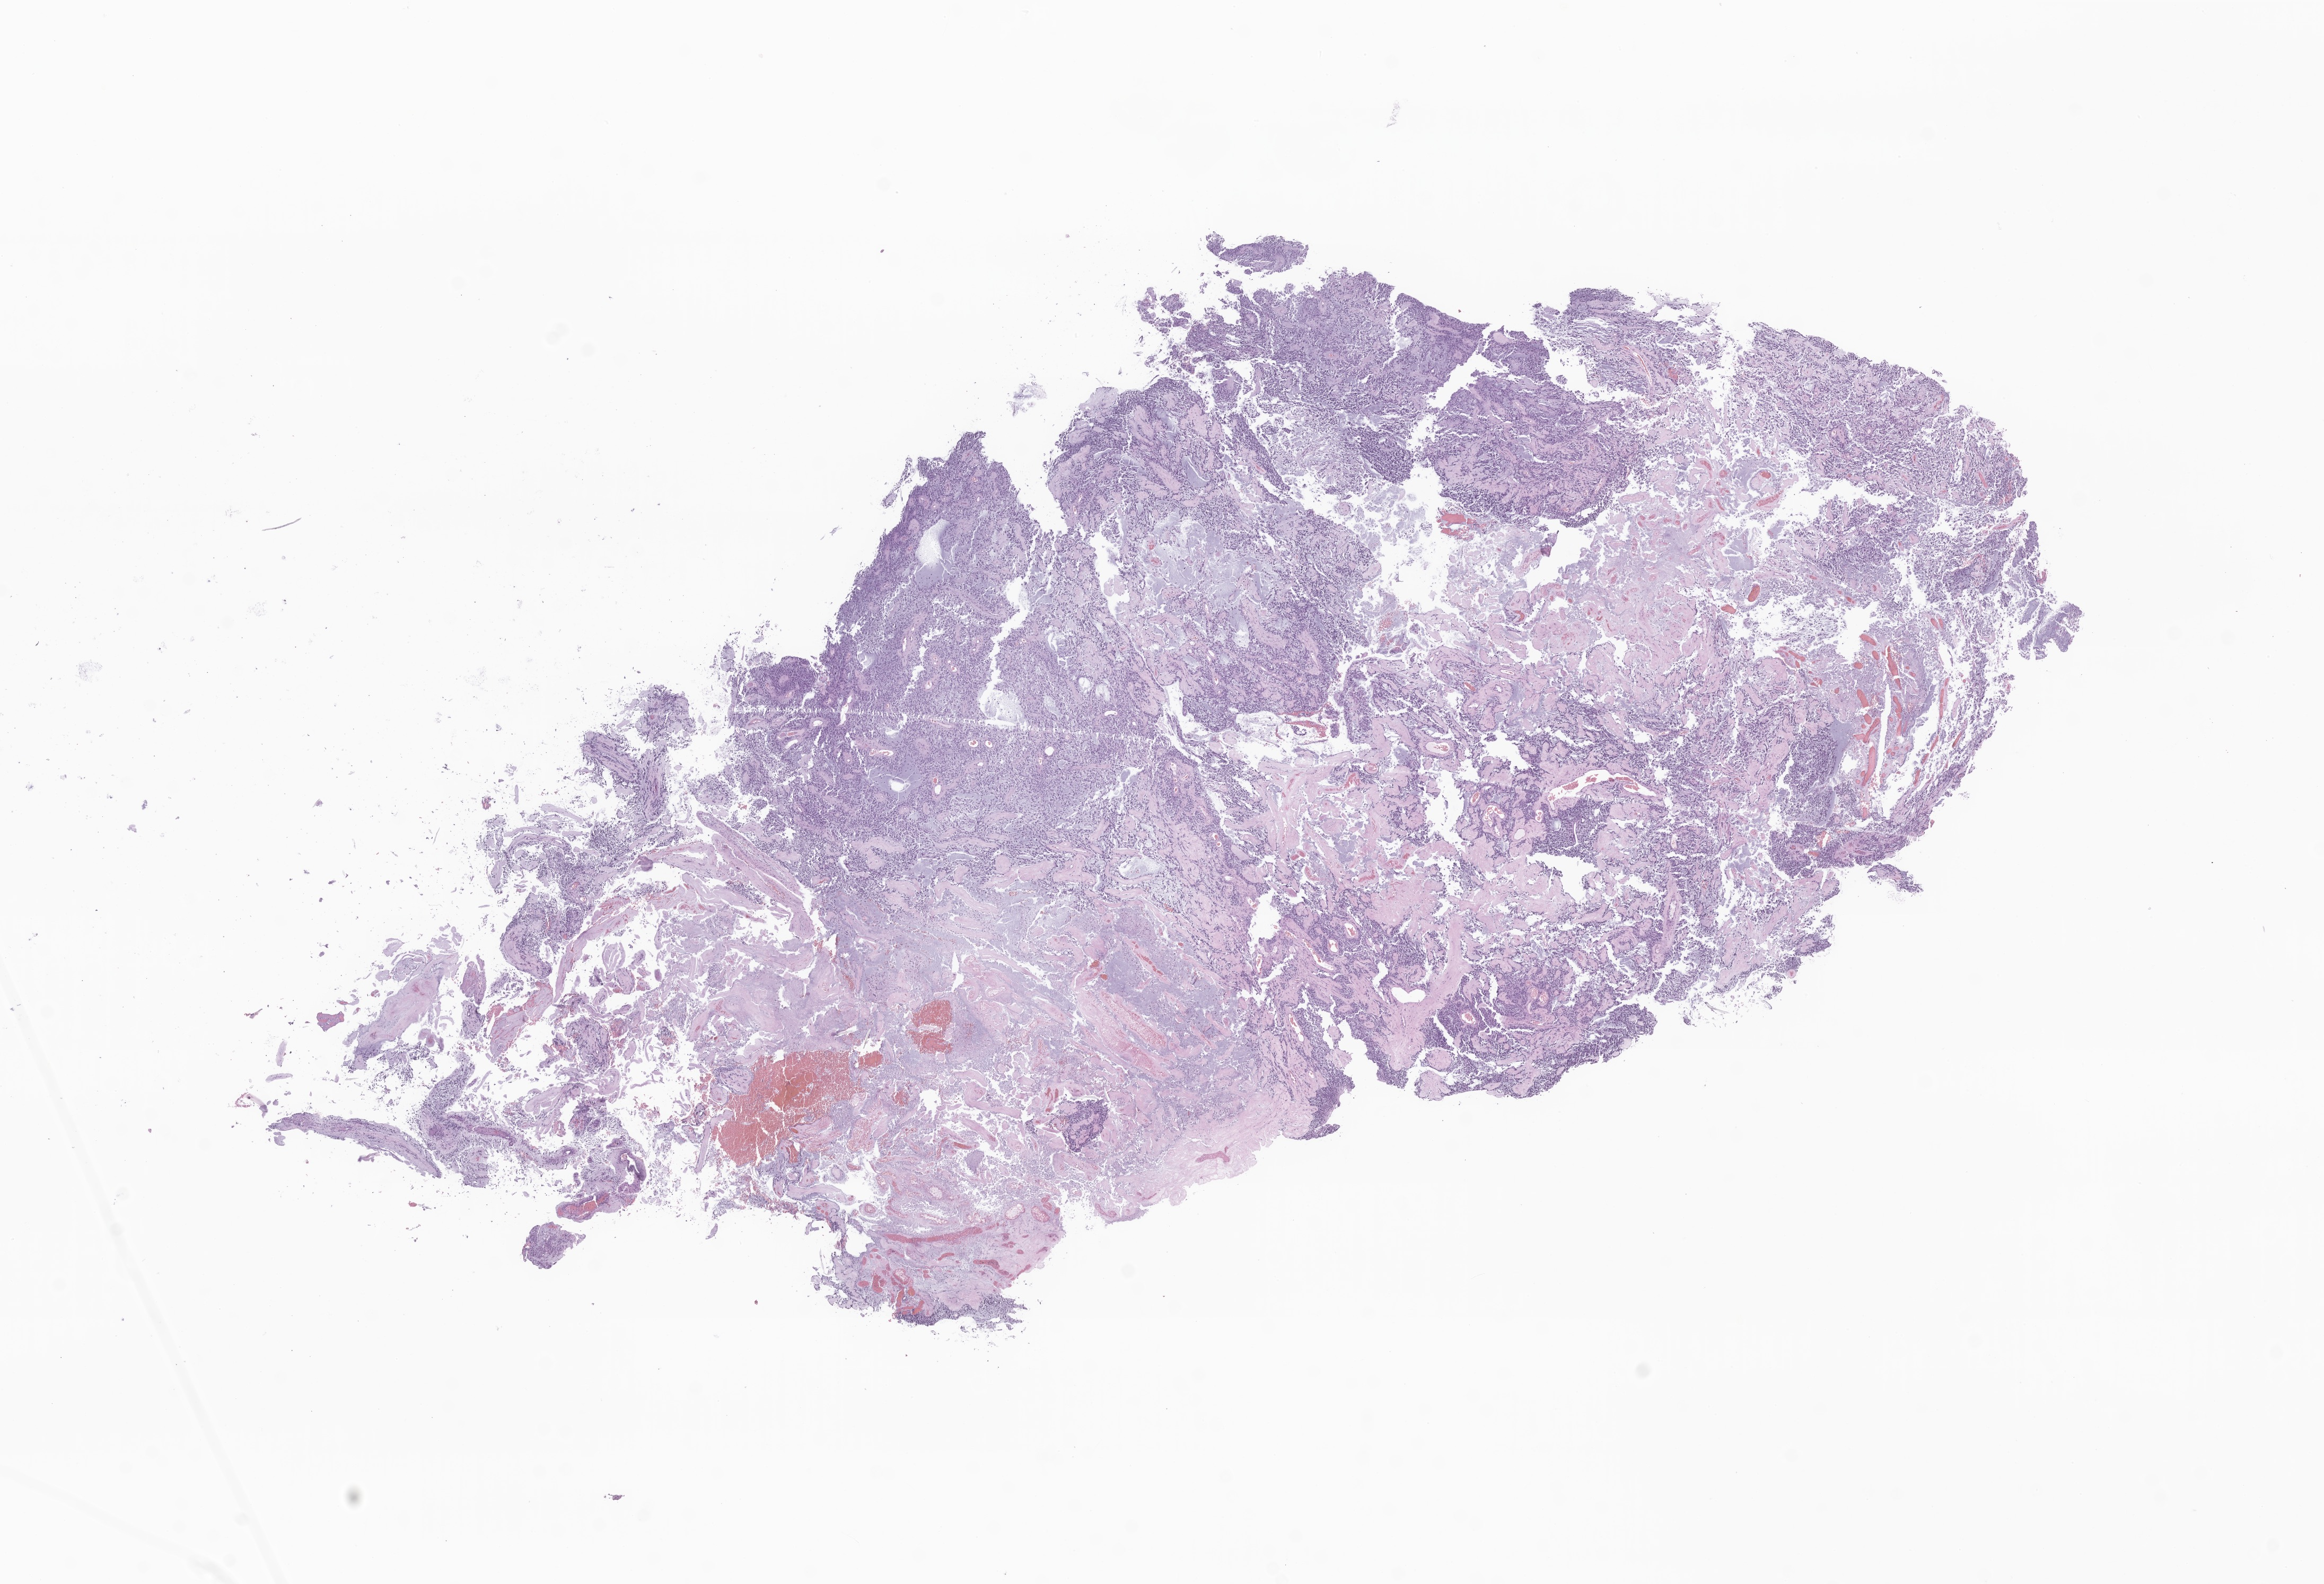
Whole-slide image, hematoxylin and eosin (H&E) stain of tumor tissue from the brain — whole scanned area (about 18.5 x 12.6 mm) shown as a low-resolution overview, formalin-fixed, paraffin-embedded (FFPE) tissue. Patient: female, age 111 months (9 years 3 months).
Diagnosis: Pilocytic astrocytoma.